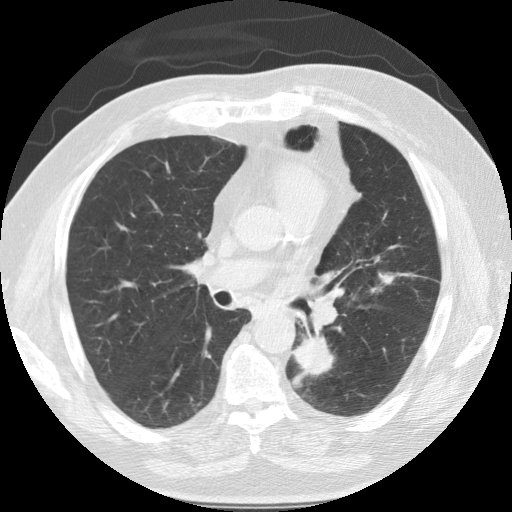
Axial slice from a low-dose chest CT screening exam, baseline annual screen, lung window (W 1500 / L -600 HU), slice 58 of 124 in the series. Male participant, aged 68 years at enrolment.
Lesion marked by an expert reader, bounding box (x1, y1, x2, y2) in pixels: (279, 317, 352, 396). The screening reader recorded 3 non-calcified nodules or masses ≥4 mm on this exam (left lower lobe, lingula, right lower lobe); which of them this box marks is not recorded. Official screen result: positive, change unspecified: nodule(s) >= 4 mm or enlarging nodule(s), mass(es), or other non-specific abnormalities suspicious for lung cancer. Participant outcome: lung cancer diagnosed 35 days after this screen — squamous cell carcinoma, NOS, left lower lobe, poorly differentiated (G3), stage IIB (AJCC 6th edition), 40 mm at pathology.